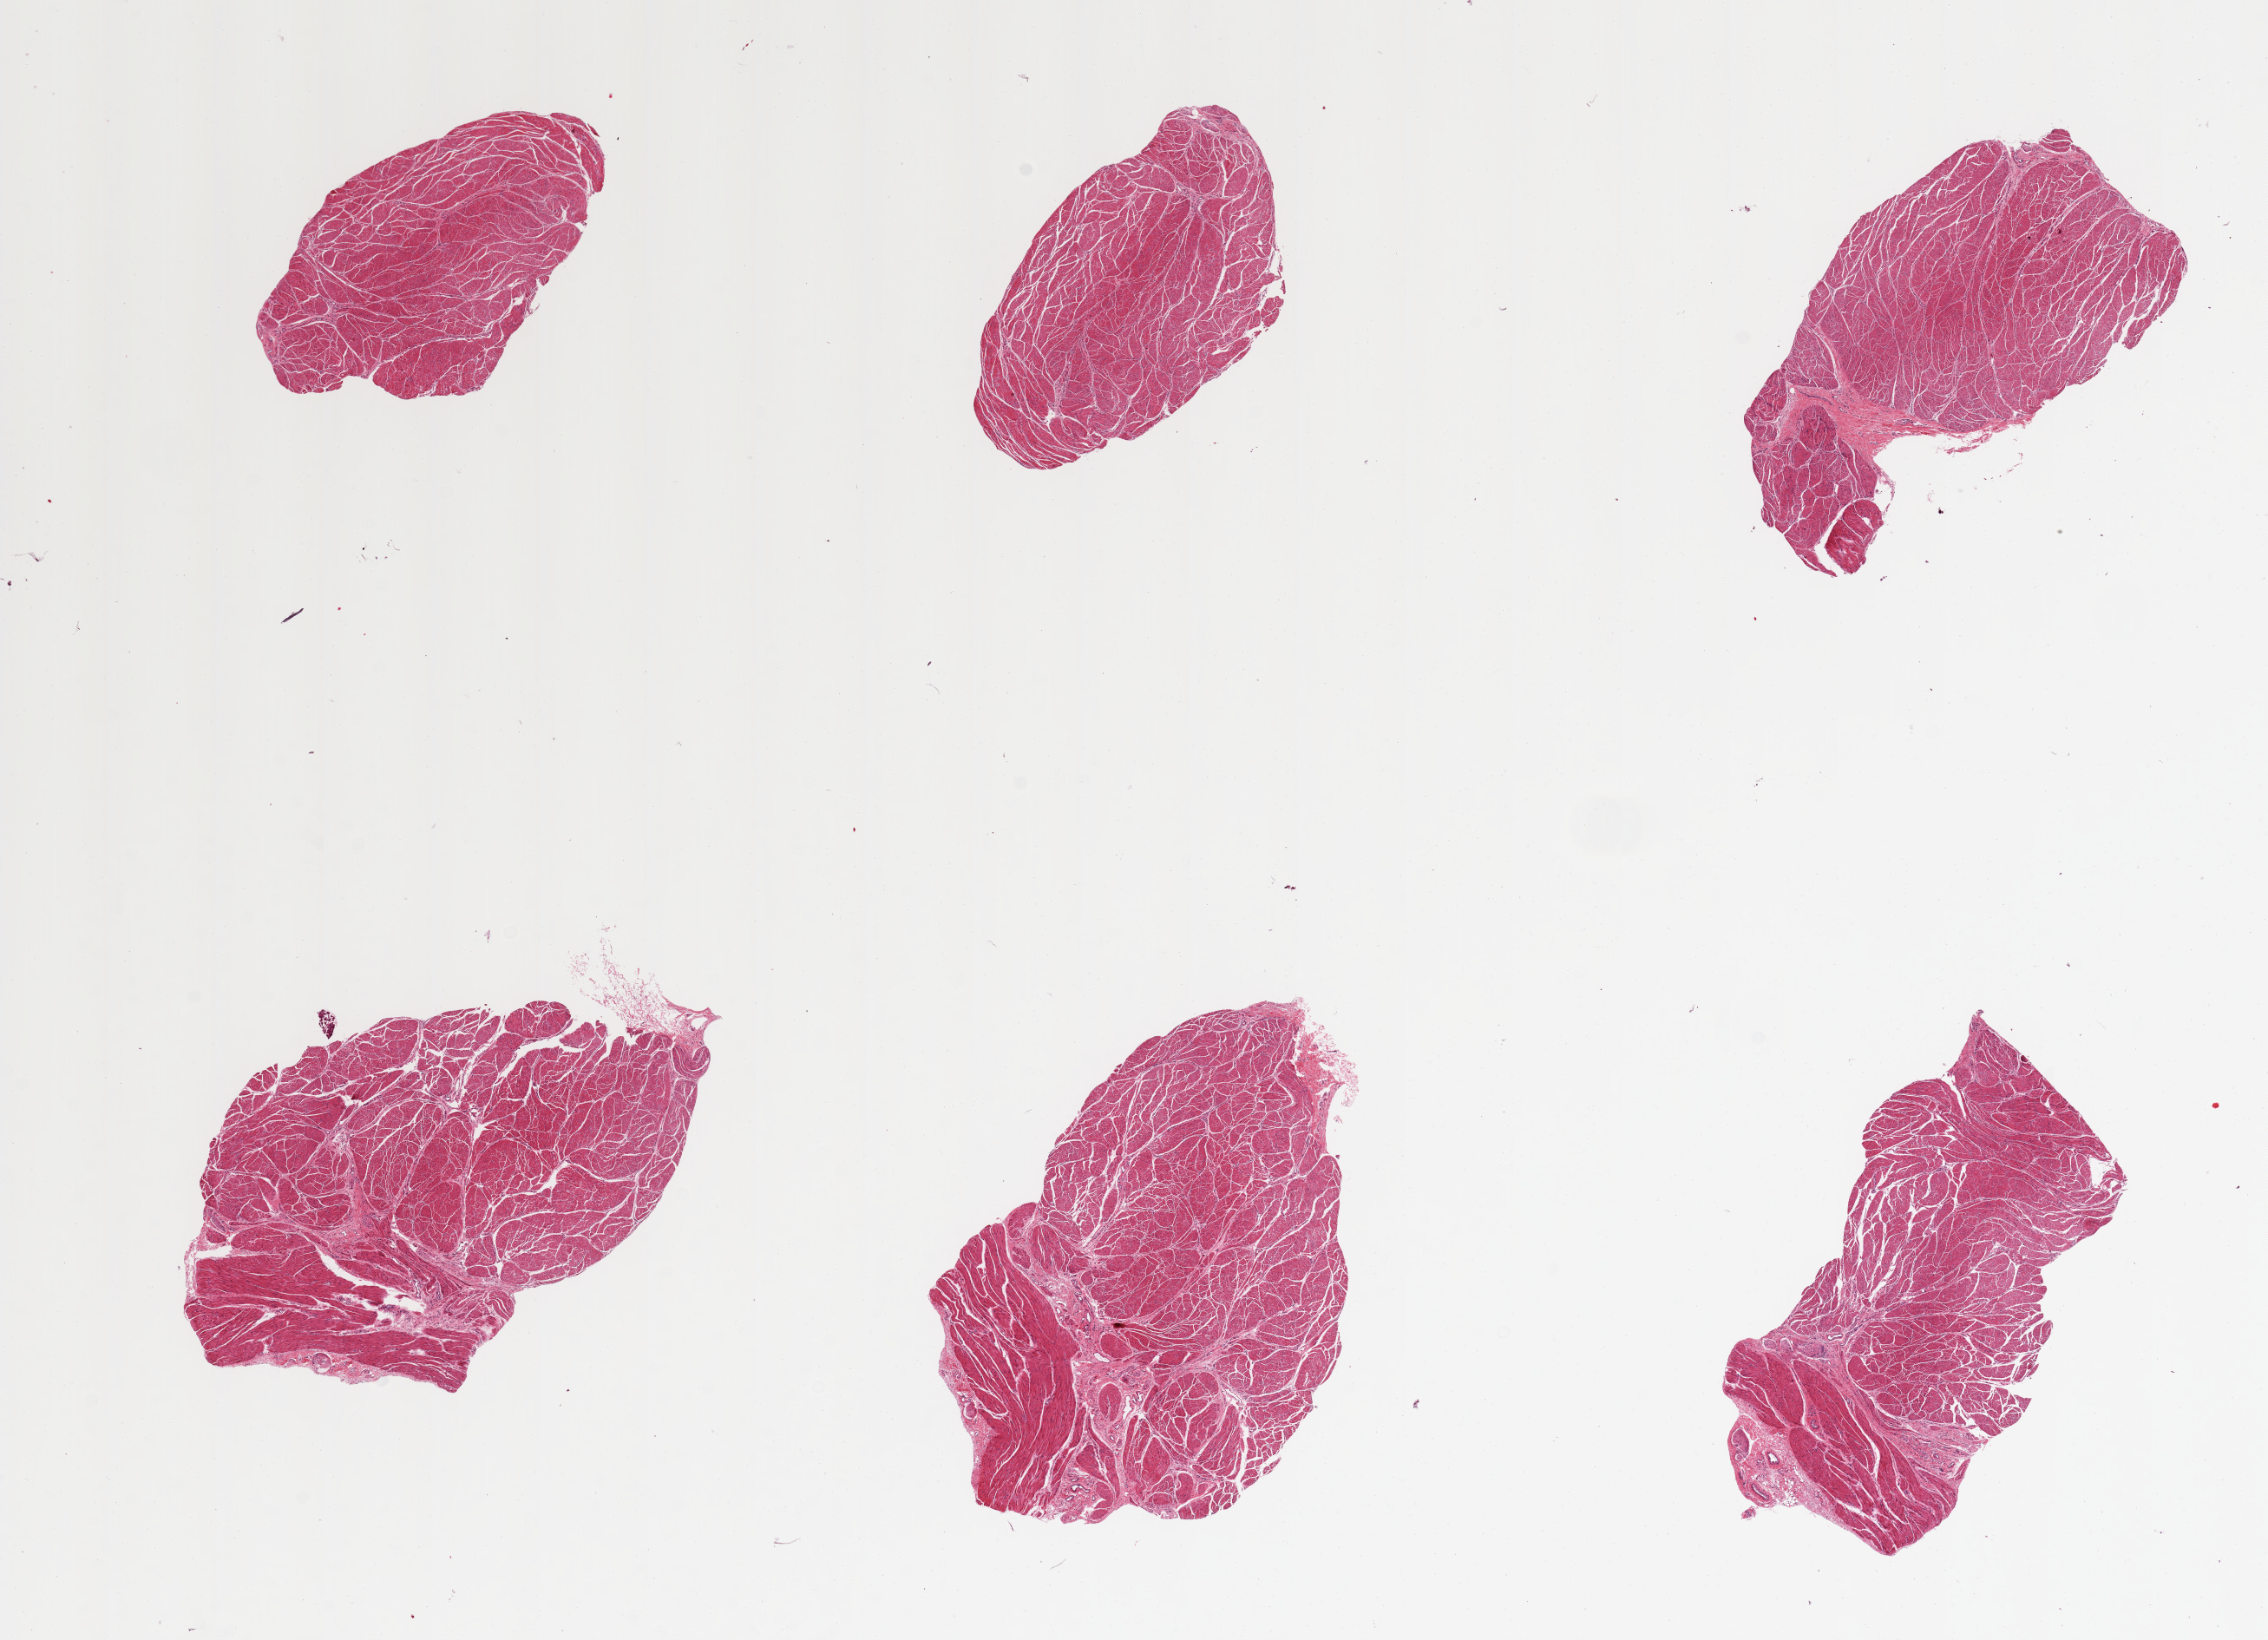
Digitized hematoxylin and eosin (H&E)-stained section — shown as a low-resolution overview of the whole scanned area (about 20.7 x 14.9 mm). PAXgene-fixed paraffin-embedded (PFPE) section. Target tissue: gastroesophageal junction. Donor tissue sample. Female donor.
Pathologist's review note for this sample: 6 pieces, well trimmed.